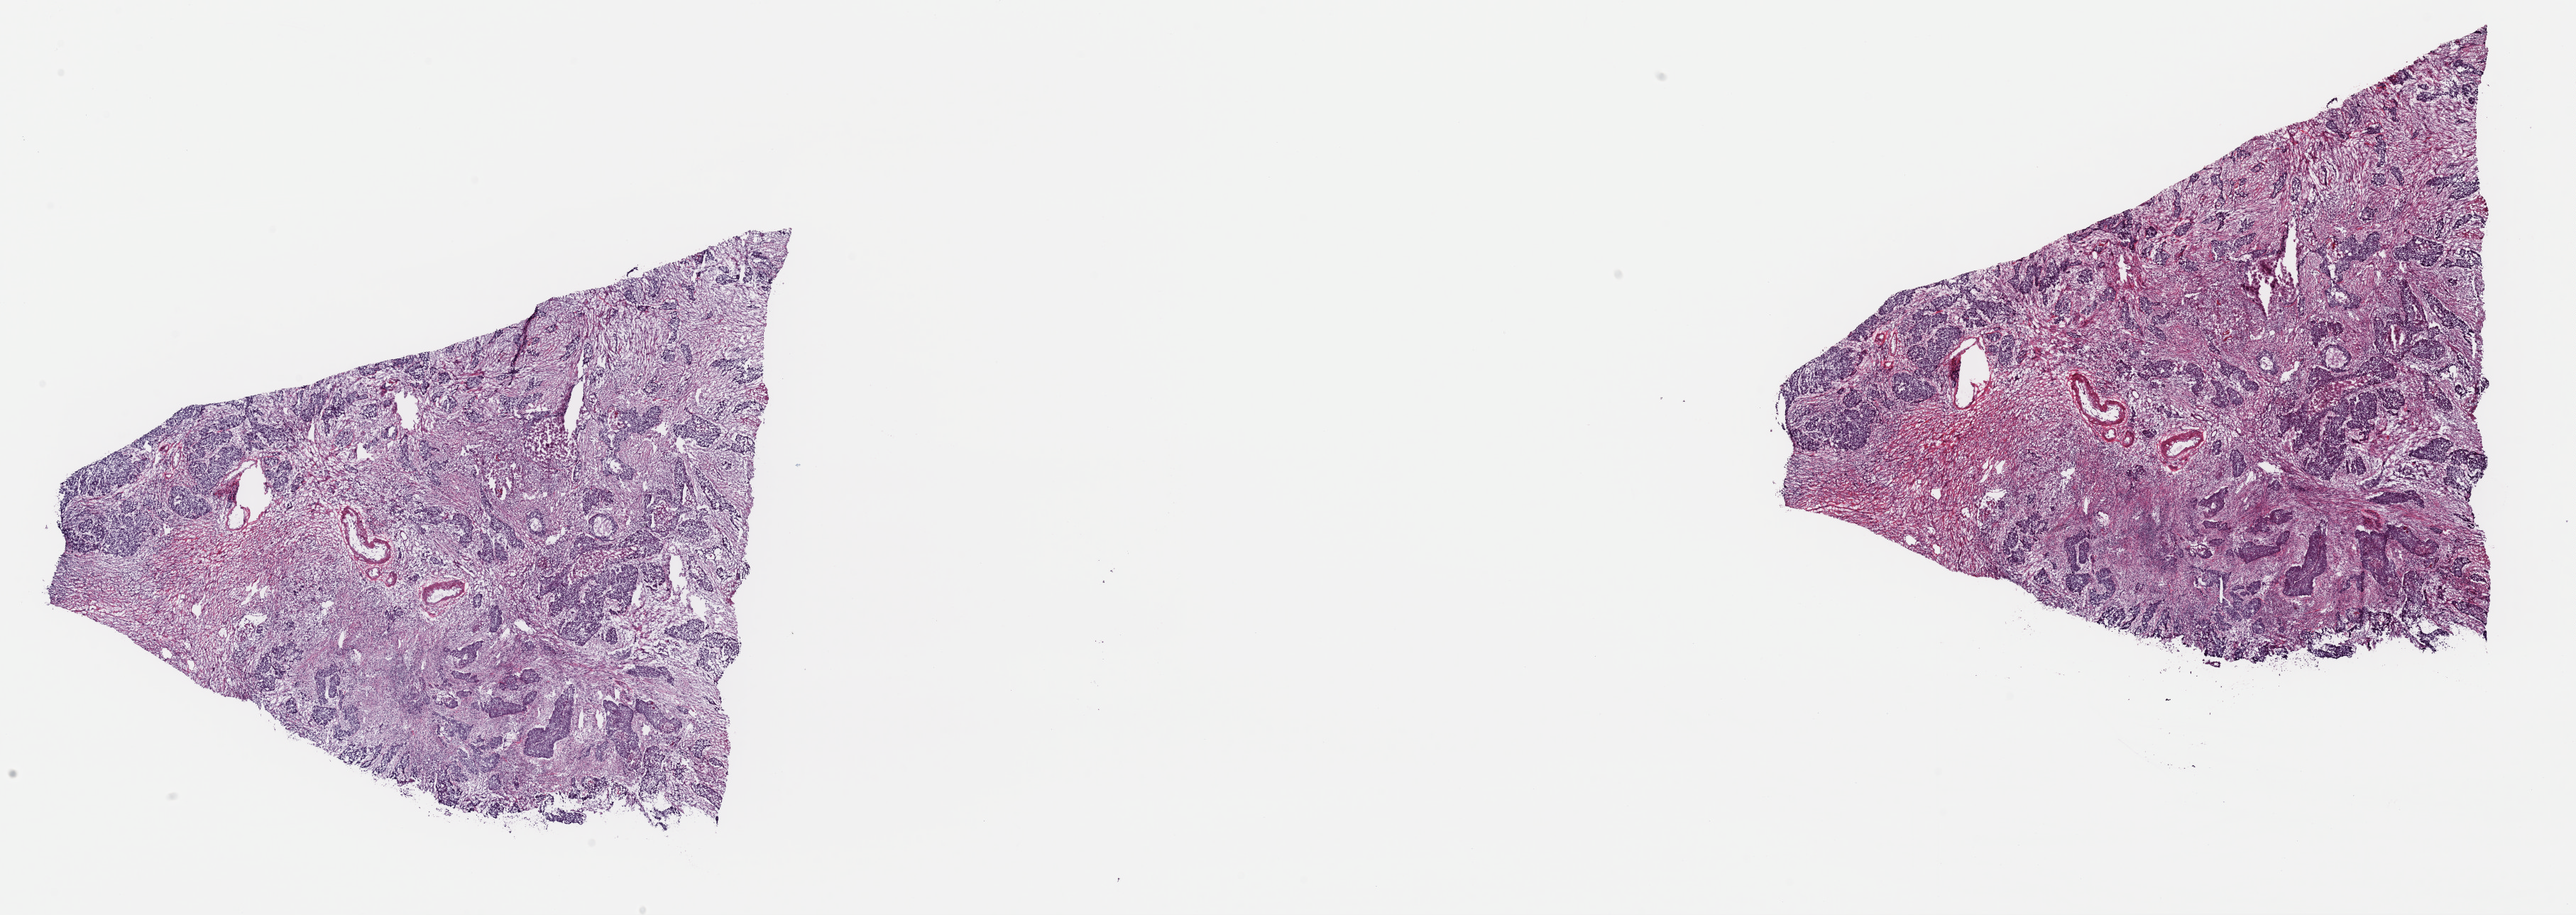
H&E-stained whole-slide image, low-resolution overview of the scanned area, about 28.7 x 10.2 mm (acquisition: 40x scan); frozen section; sample: primary tumour, bladder. Patient: female, age at initial diagnosis 70 years. Histologic grade: high grade. Slide review estimates, as recorded: tumour cells 80%, tumour nuclei 65%, normal cells 0%, stromal cells 15%, necrosis 5%. Infiltration values recorded for this section: lymphocyte infiltration 0%, monocyte infiltration 0%, neutrophil infiltration 0%.
• diagnosis: Transitional cell carcinoma (trigone of bladder)
• AJCC pathologic stage: III